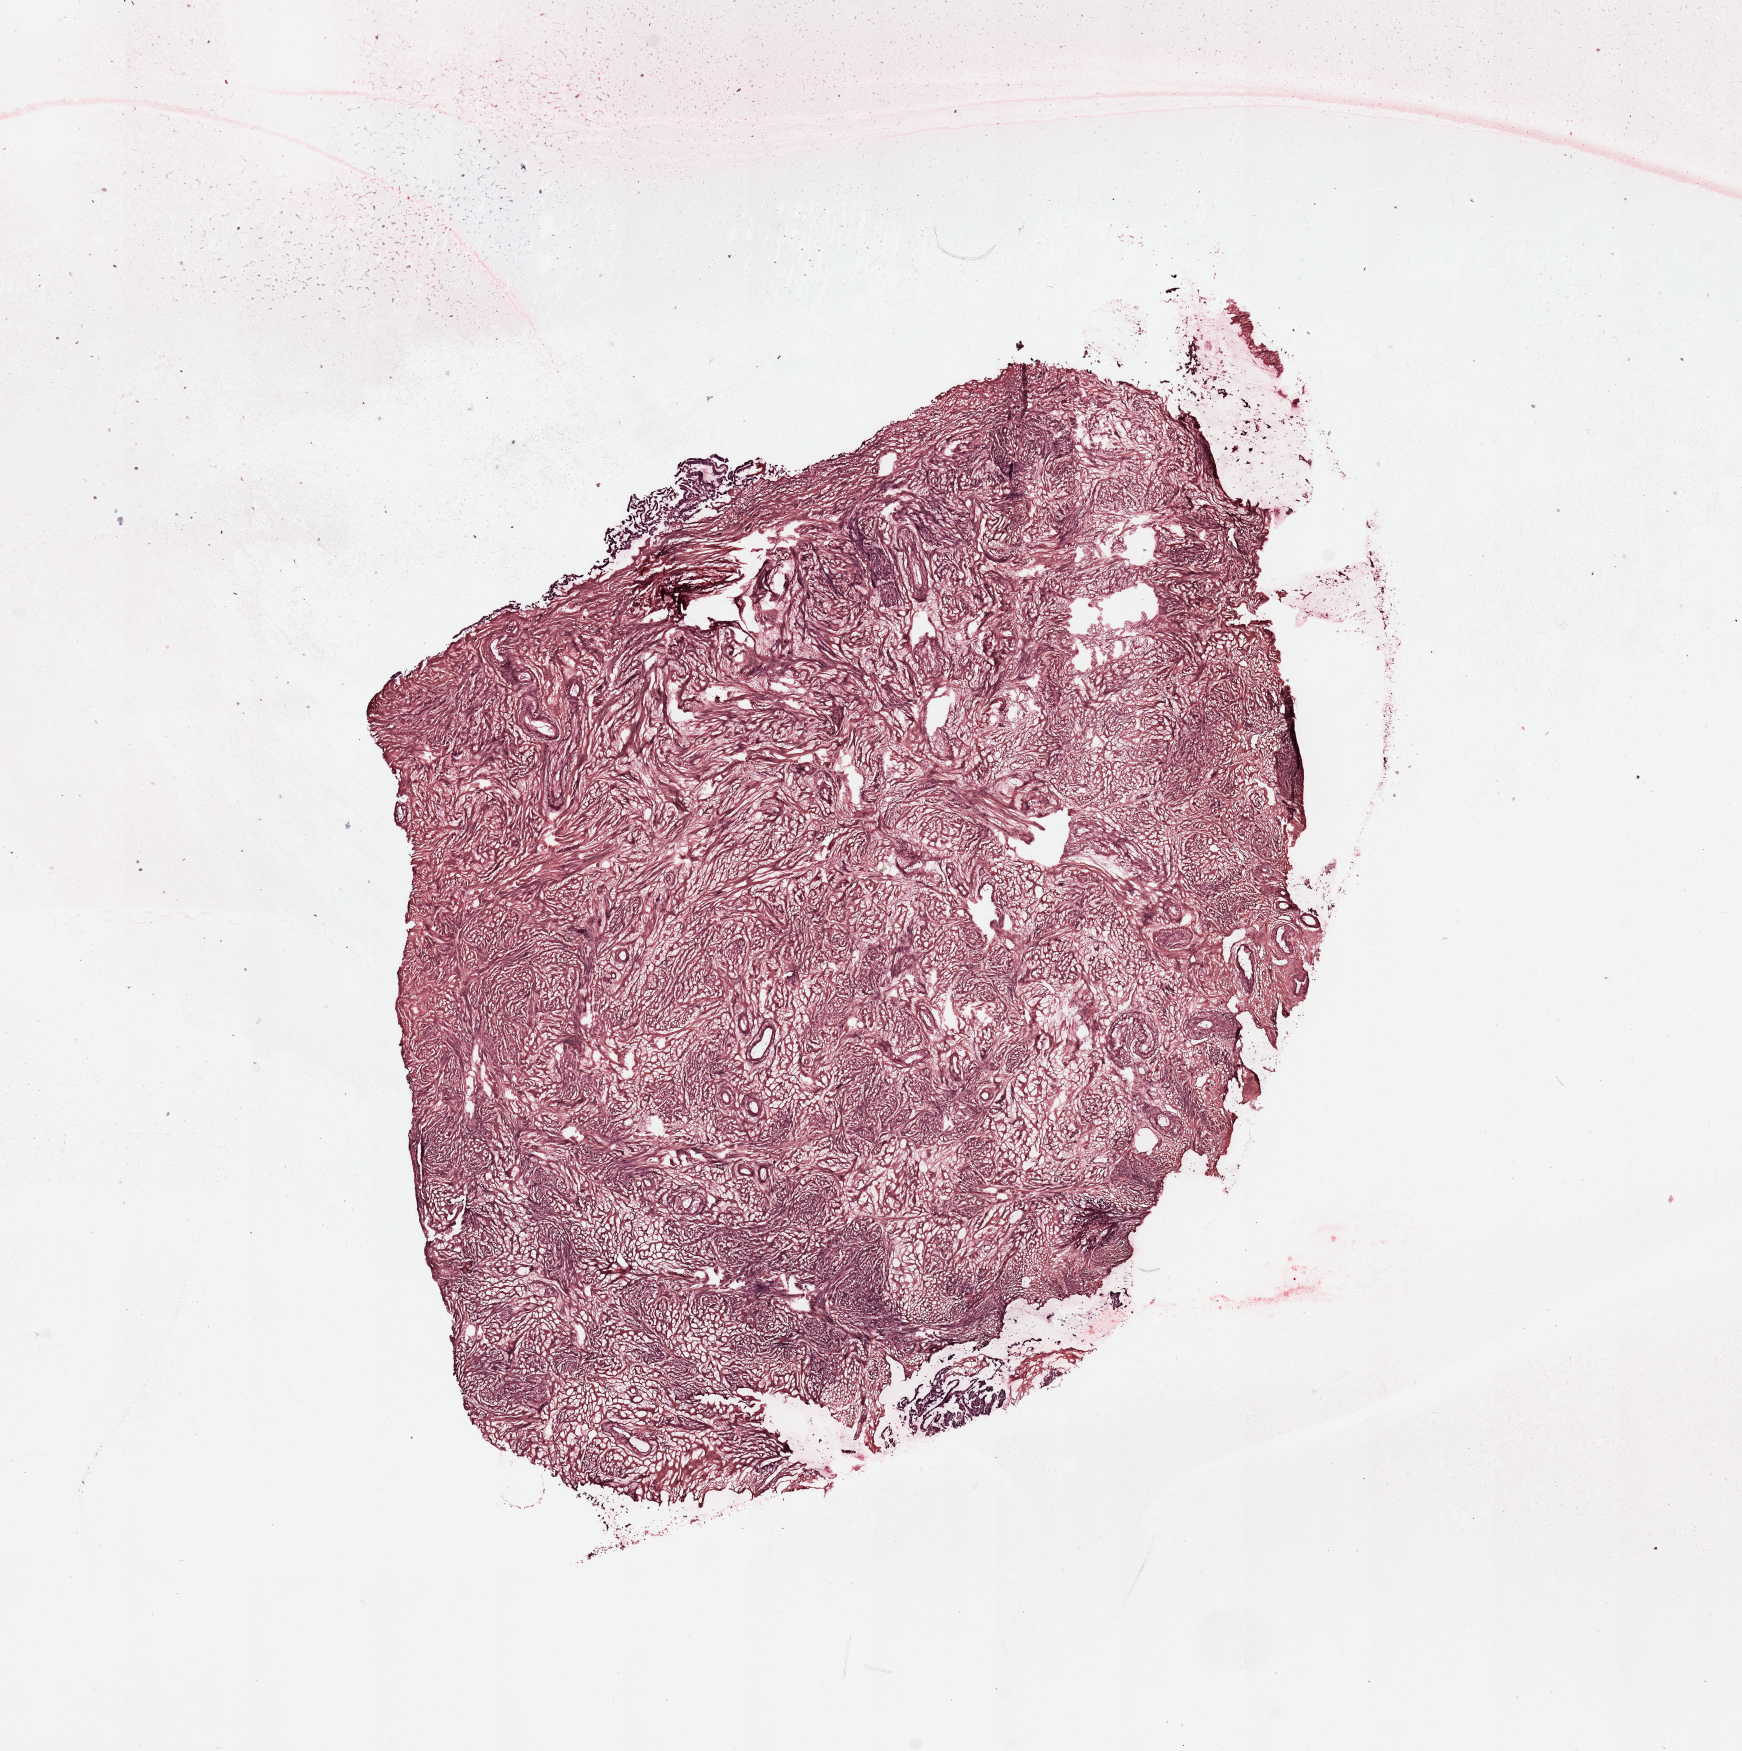
H&E-stained whole-slide image, whole scanned area (about 13.8 x 13.9 mm) shown as a low-resolution overview, uterus, normal (non-tumour) tissue. Female, 64 y/o.
This section: normal (non-tumour) tissue from the same patient. Patient diagnosis: Endometrioid adenocarcinoma, NOS.